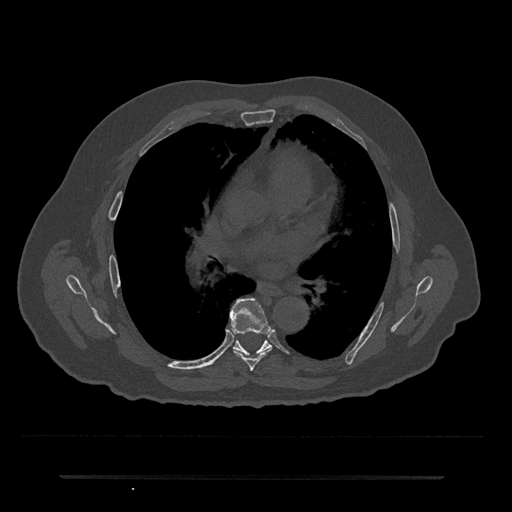
CT including the spine, one axial slice. Slice 416 of 797 in the series (ordered by position). Reconstruction kernel Br40s/3. 120 kVp. Bone window (W 1800 / L 400 HU). 0.5 mm slice thickness. 512 × 512 image matrix, field of view 437 × 437 mm. Male patient, age 69 years. From the clinical record (not read from this slice): primary cancer: prostate.
Annotated regions visible in this slice (semi-automatically segmented with operator editing):
- T6 vertebra: bounding box <230,299,273,371> (left, top, right, bottom; pixels)
- T7 vertebra: <233,340,271,356>